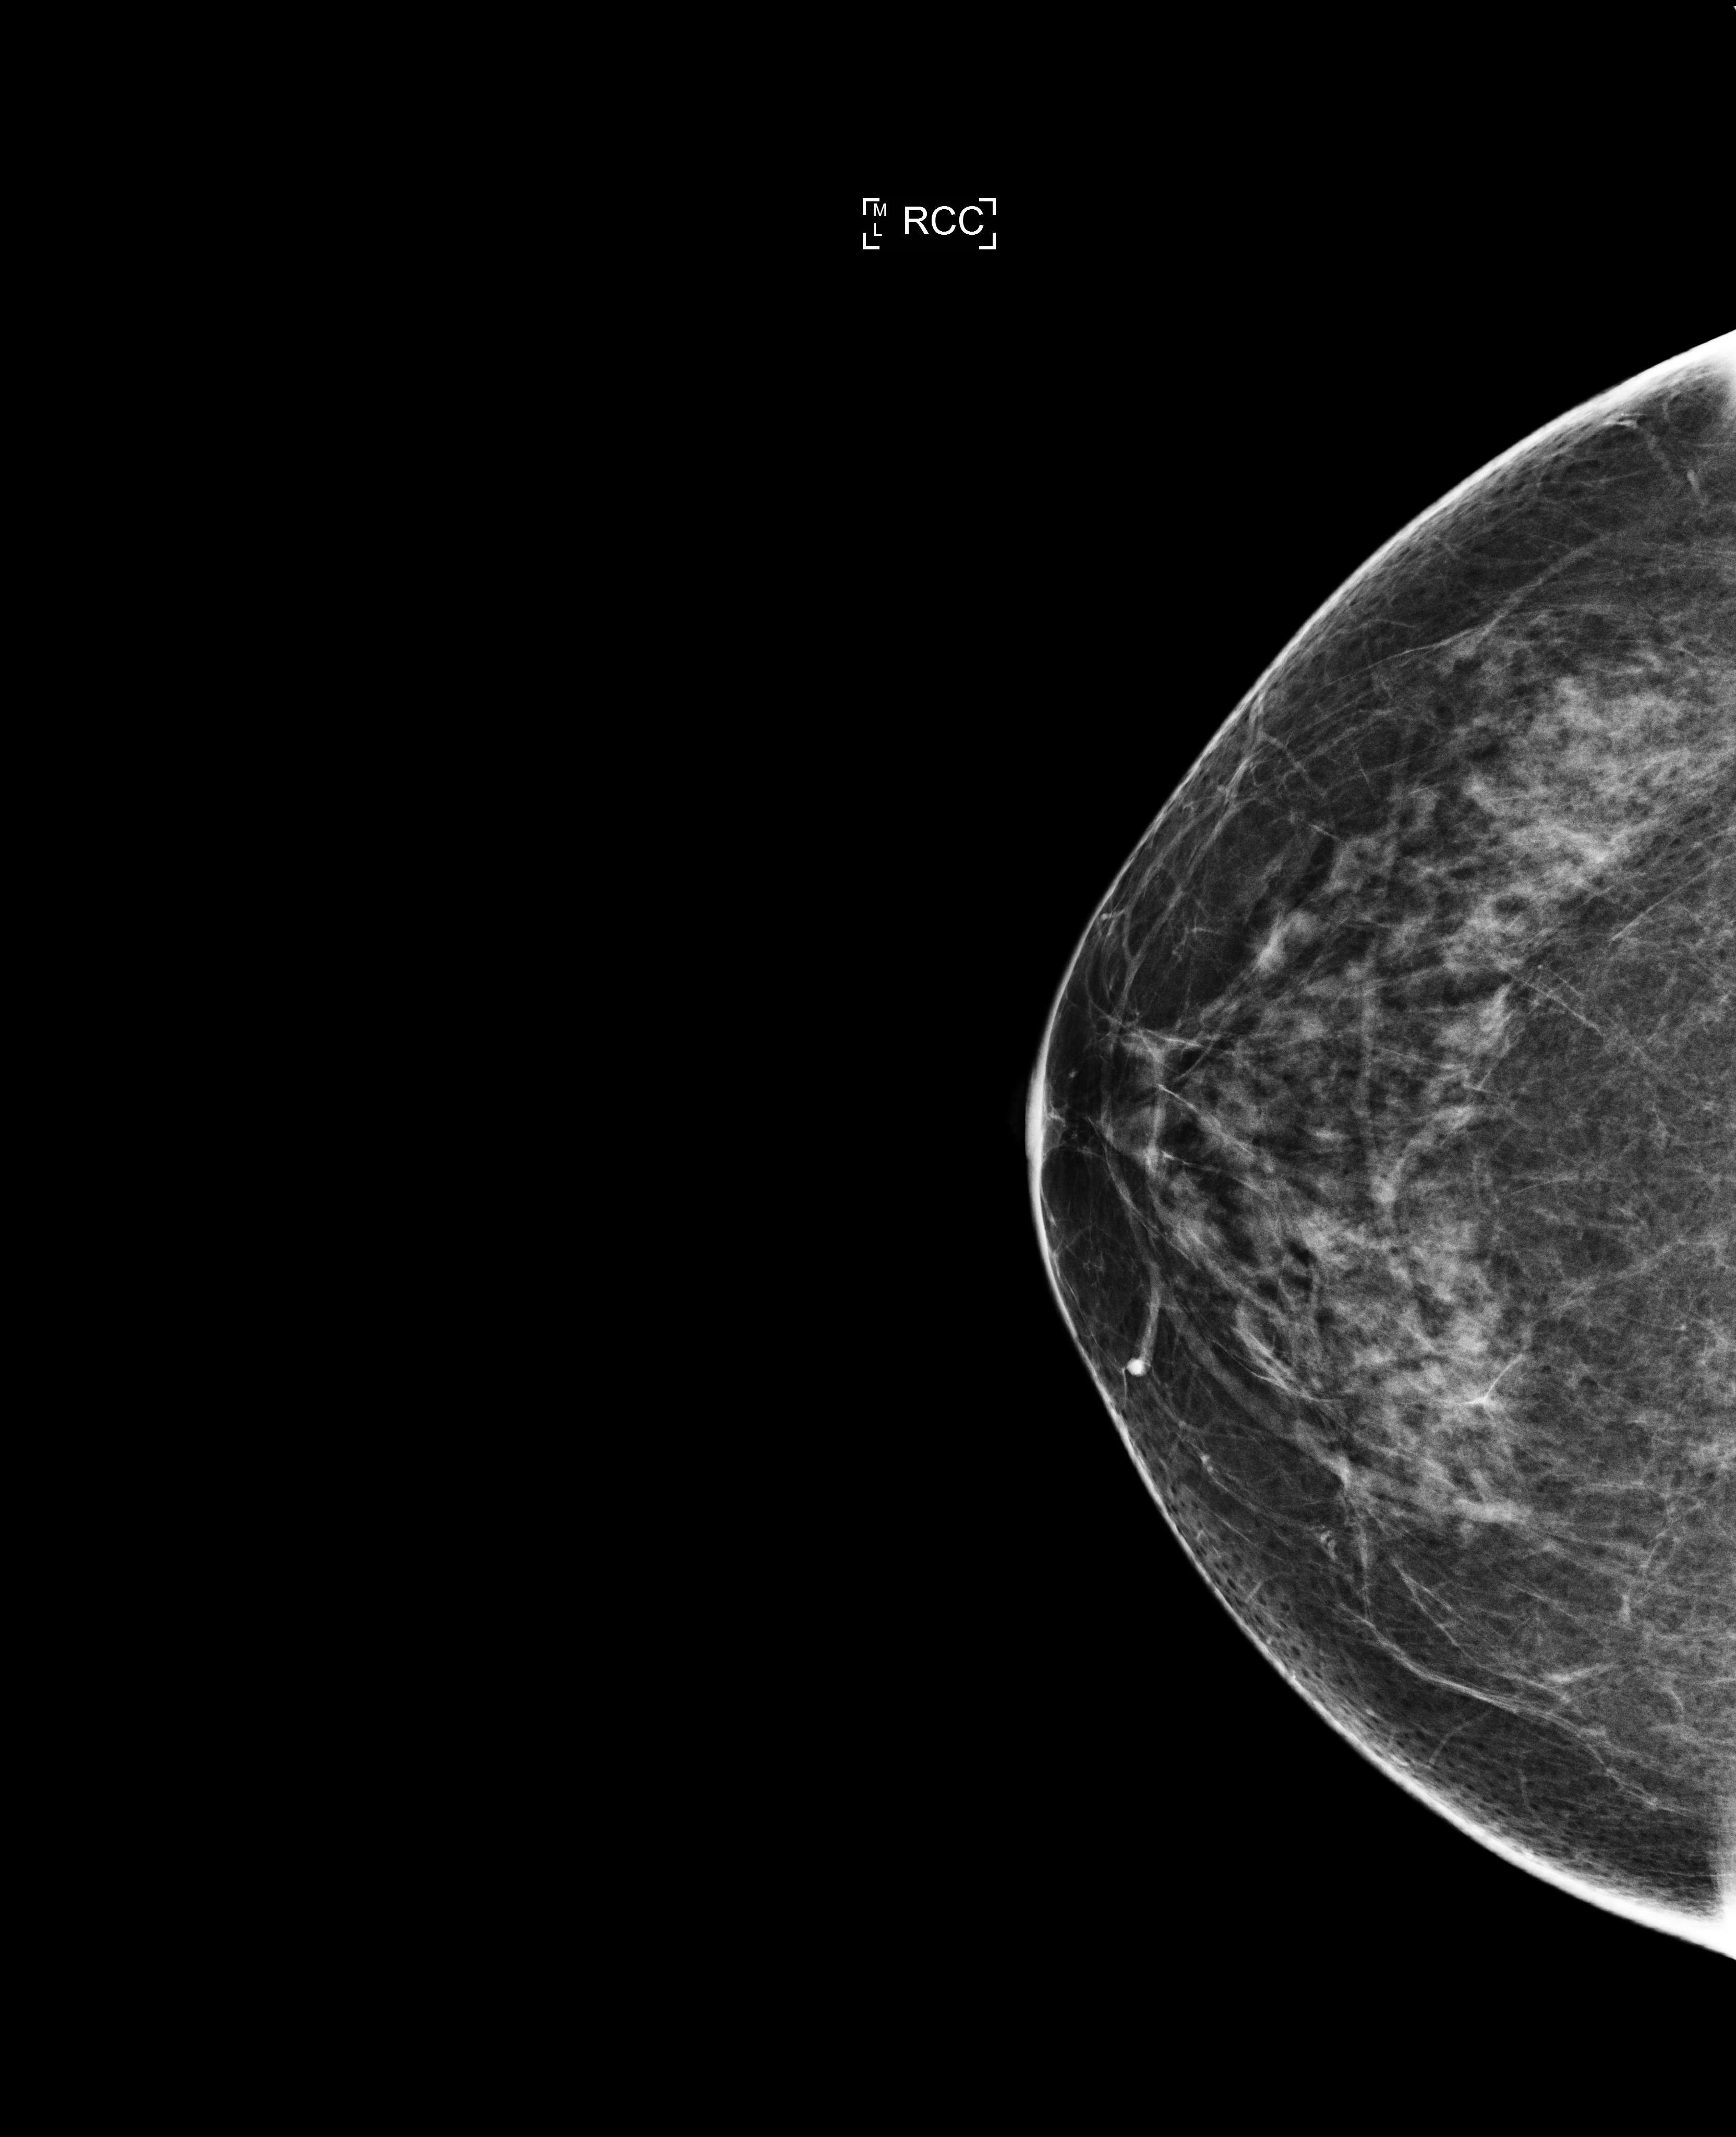
Digital mammogram (FFDM), right breast, craniocaudal (CC) view, screening examination, compressed breast thickness 58 mm. Patient aged 56 years (female).
- breast density at the screening exam (both breasts): scattered fibroglandular densities (BI-RADS density category b)
- final BI-RADS assessment for this screening round (tomosynthesis exam, both breasts): category 1
- recall: no recall after this screen